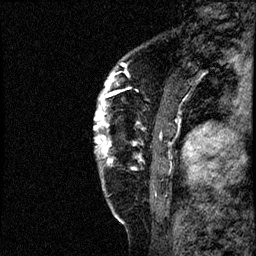
Breast MRI (dynamic contrast-enhanced), one sagittal slice; slice 11 of 60 in the series (ordered by position); dynamic contrast-enhanced study with each time point stored as its own series, time point 2 of 4 at this slice position (early post-contrast, ordered by acquisition time); 1.5 T; TE 4.2 ms, TR 17.6 ms; 2 mm slice thickness; 256 × 256 image matrix, field of view 200 × 200 mm. Female patient, age 40 years. From the clinical record (not read from this slice): setting: breast cancer imaged before/during neoadjuvant chemotherapy; receptor status: HER2-positive.
Structures marked on this image (semi-automatic segmentation, software-assisted and operator-edited):
- analysis volume of interest (the breast-tissue region the enhancement analysis was run in; not a lesion): bounding box (x1, y1, x2, y2) in pixels: (95, 56, 197, 205)
- tumour enhancement mask (voxels above the 100 % enhancement threshold inside the analysis volume of interest): (95, 63, 172, 169)